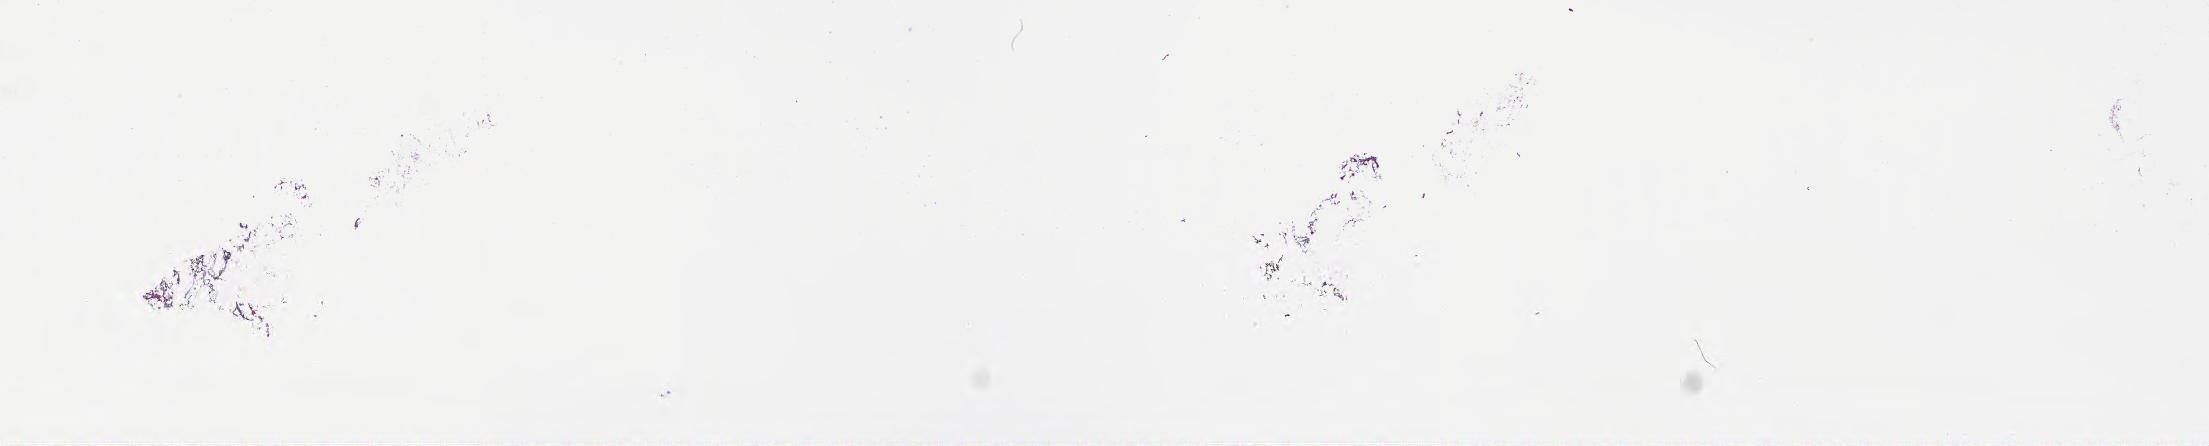
Digitized H&E-stained section of tumor tissue from the brain — shown as a low-resolution overview of the whole scanned area (about 35.7 x 7.2 mm); cryosection (OCT / tissue freezing medium). Patient: female, age 122 months.
Diagnosis (ICD-O-3 morphology term): Astrocytoma, NOS.